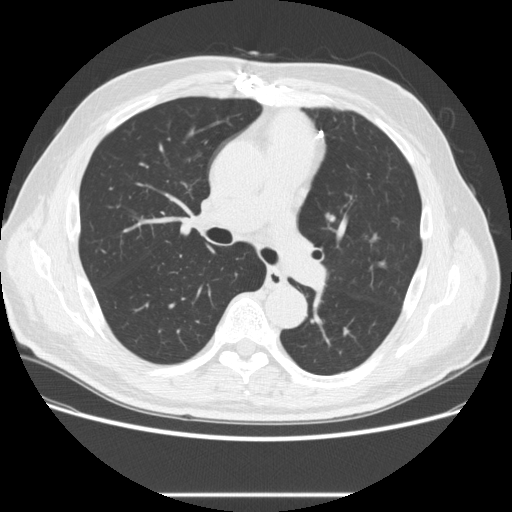
Axial slice from a low-dose chest CT screening exam. Second screening round (one year after baseline). Lung window (W 1500 / L -600 HU). 2.5 mm slice thickness. Slice 94 of 268 in the series. 512 × 512 image matrix. Male participant, aged 66 years at enrolment. Former smoker at enrolment.
Expert-annotated lung lesion, bounding box <319,200,350,232> (left, top, right, bottom; pixels). Reader record for this screening exam (exam-level; its link to the box is not recorded): non-calcified nodule or mass ≥4 mm, right lower lobe, 4 × 4 mm, smooth margins, soft tissue attenuation, pre-existing on the prior screen: yes; interval growth: no. Note: the box lies in the patient's left hemithorax on this image, whereas the reader's record names the right lung; they may be different findings. Official screen result: positive, no significant change: stable abnormalities potentially related to lung cancer, unchanged since the prior screening exam. Lung cancer was diagnosed 449 days after this screen: squamous cell carcinoma, NOS, left upper lobe, poorly differentiated (G3), stage IA (AJCC 6th edition), 27 mm at pathology.